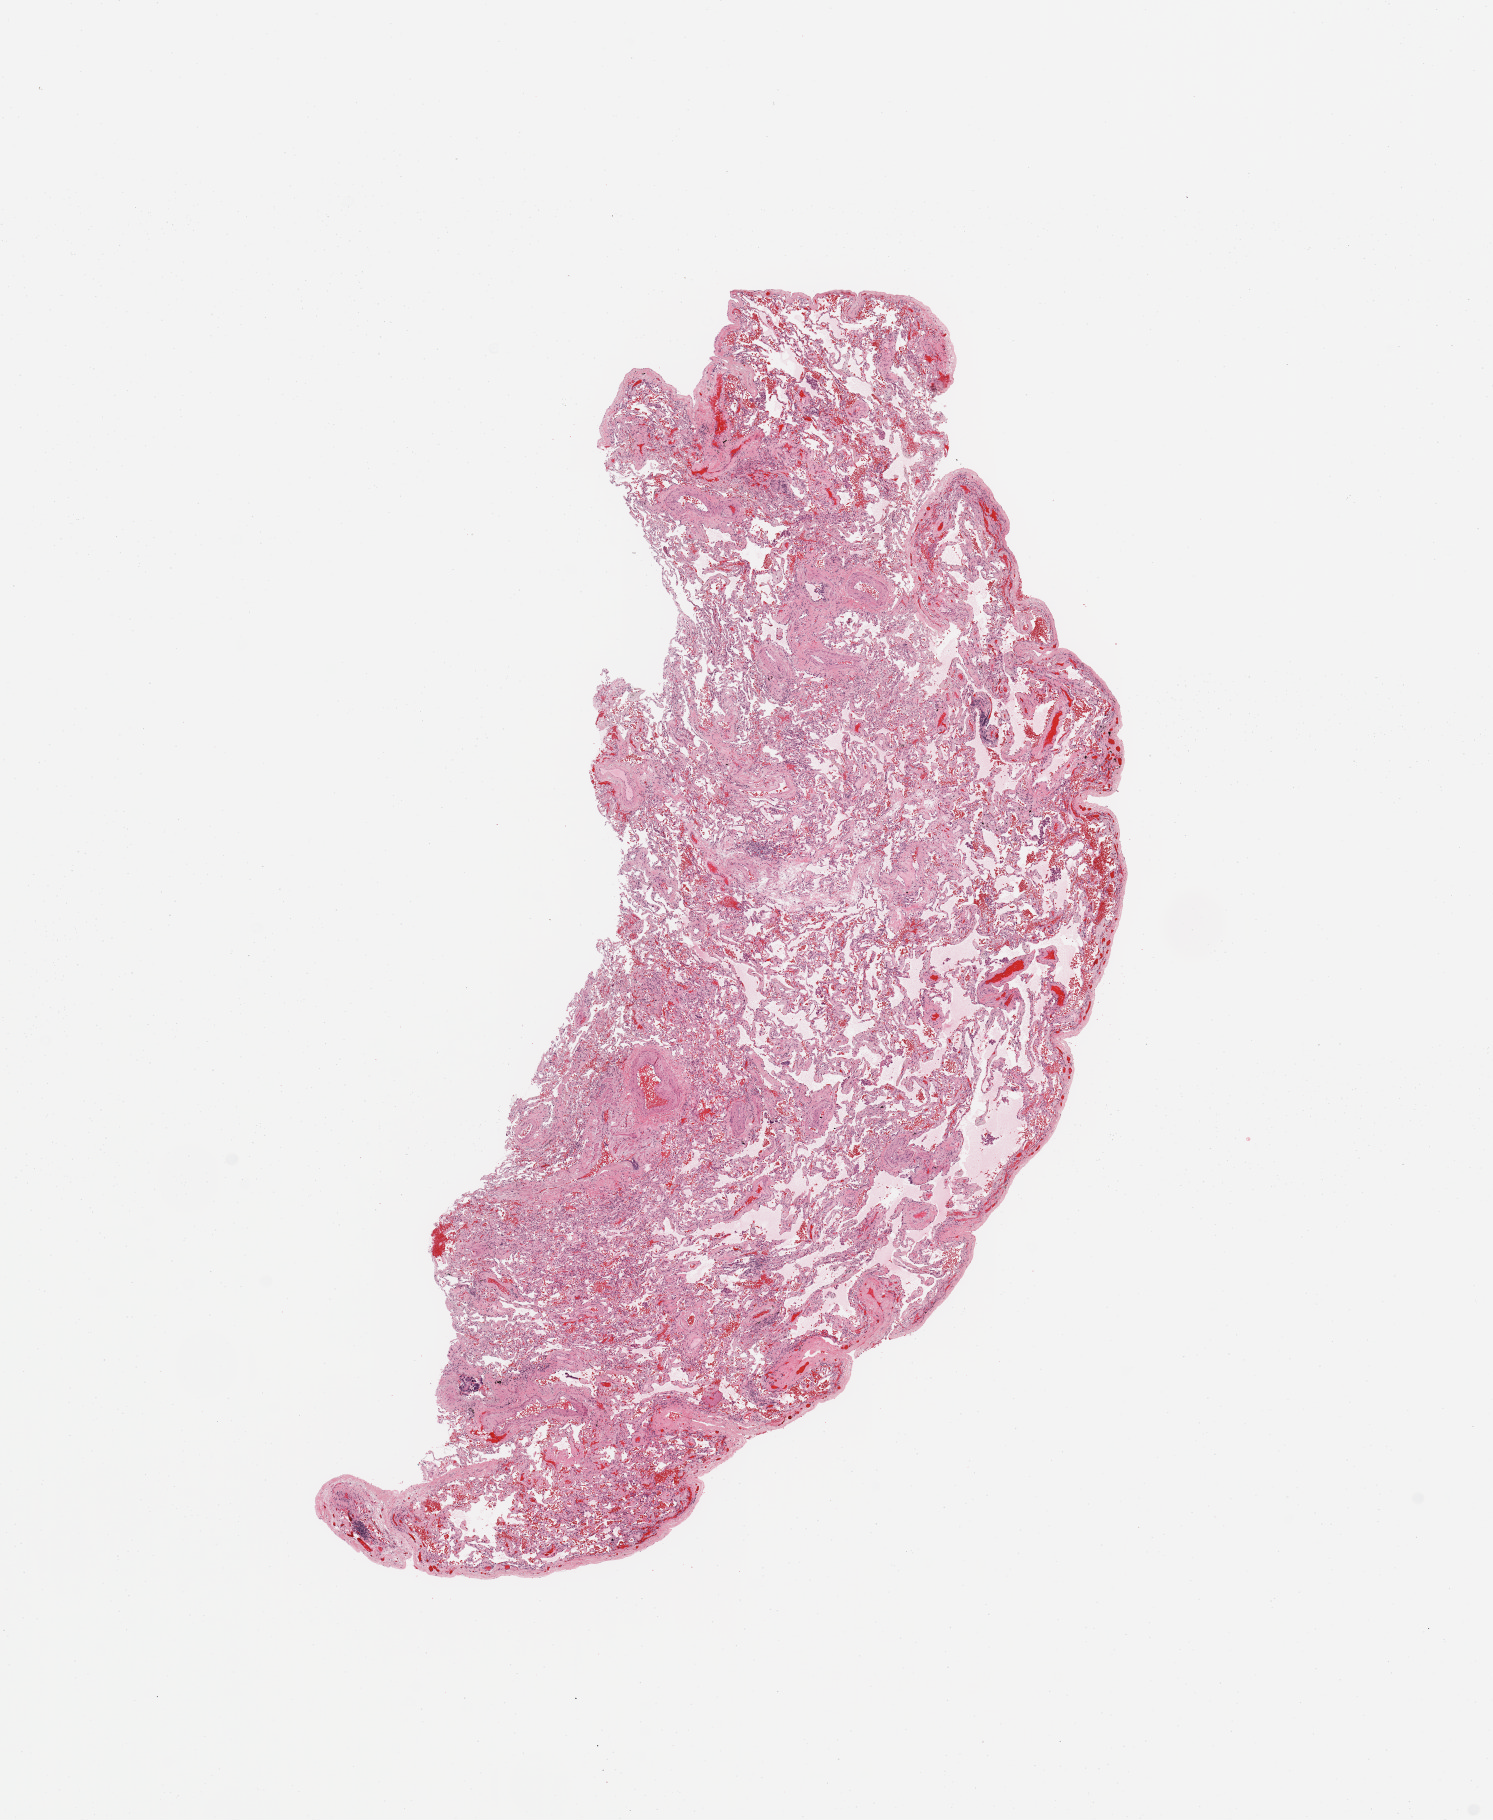
H&E whole-slide image, low-resolution overview of the scanned area, about 11.8 x 14.4 mm (slide scanned at 20x). Normal (non-tumour) tissue sample, sampled site: lung. Patient: male, age 72 years.
This section: normal (non-tumour) tissue from the same patient. Patient diagnosis: Squamous cell carcinoma, NOS.